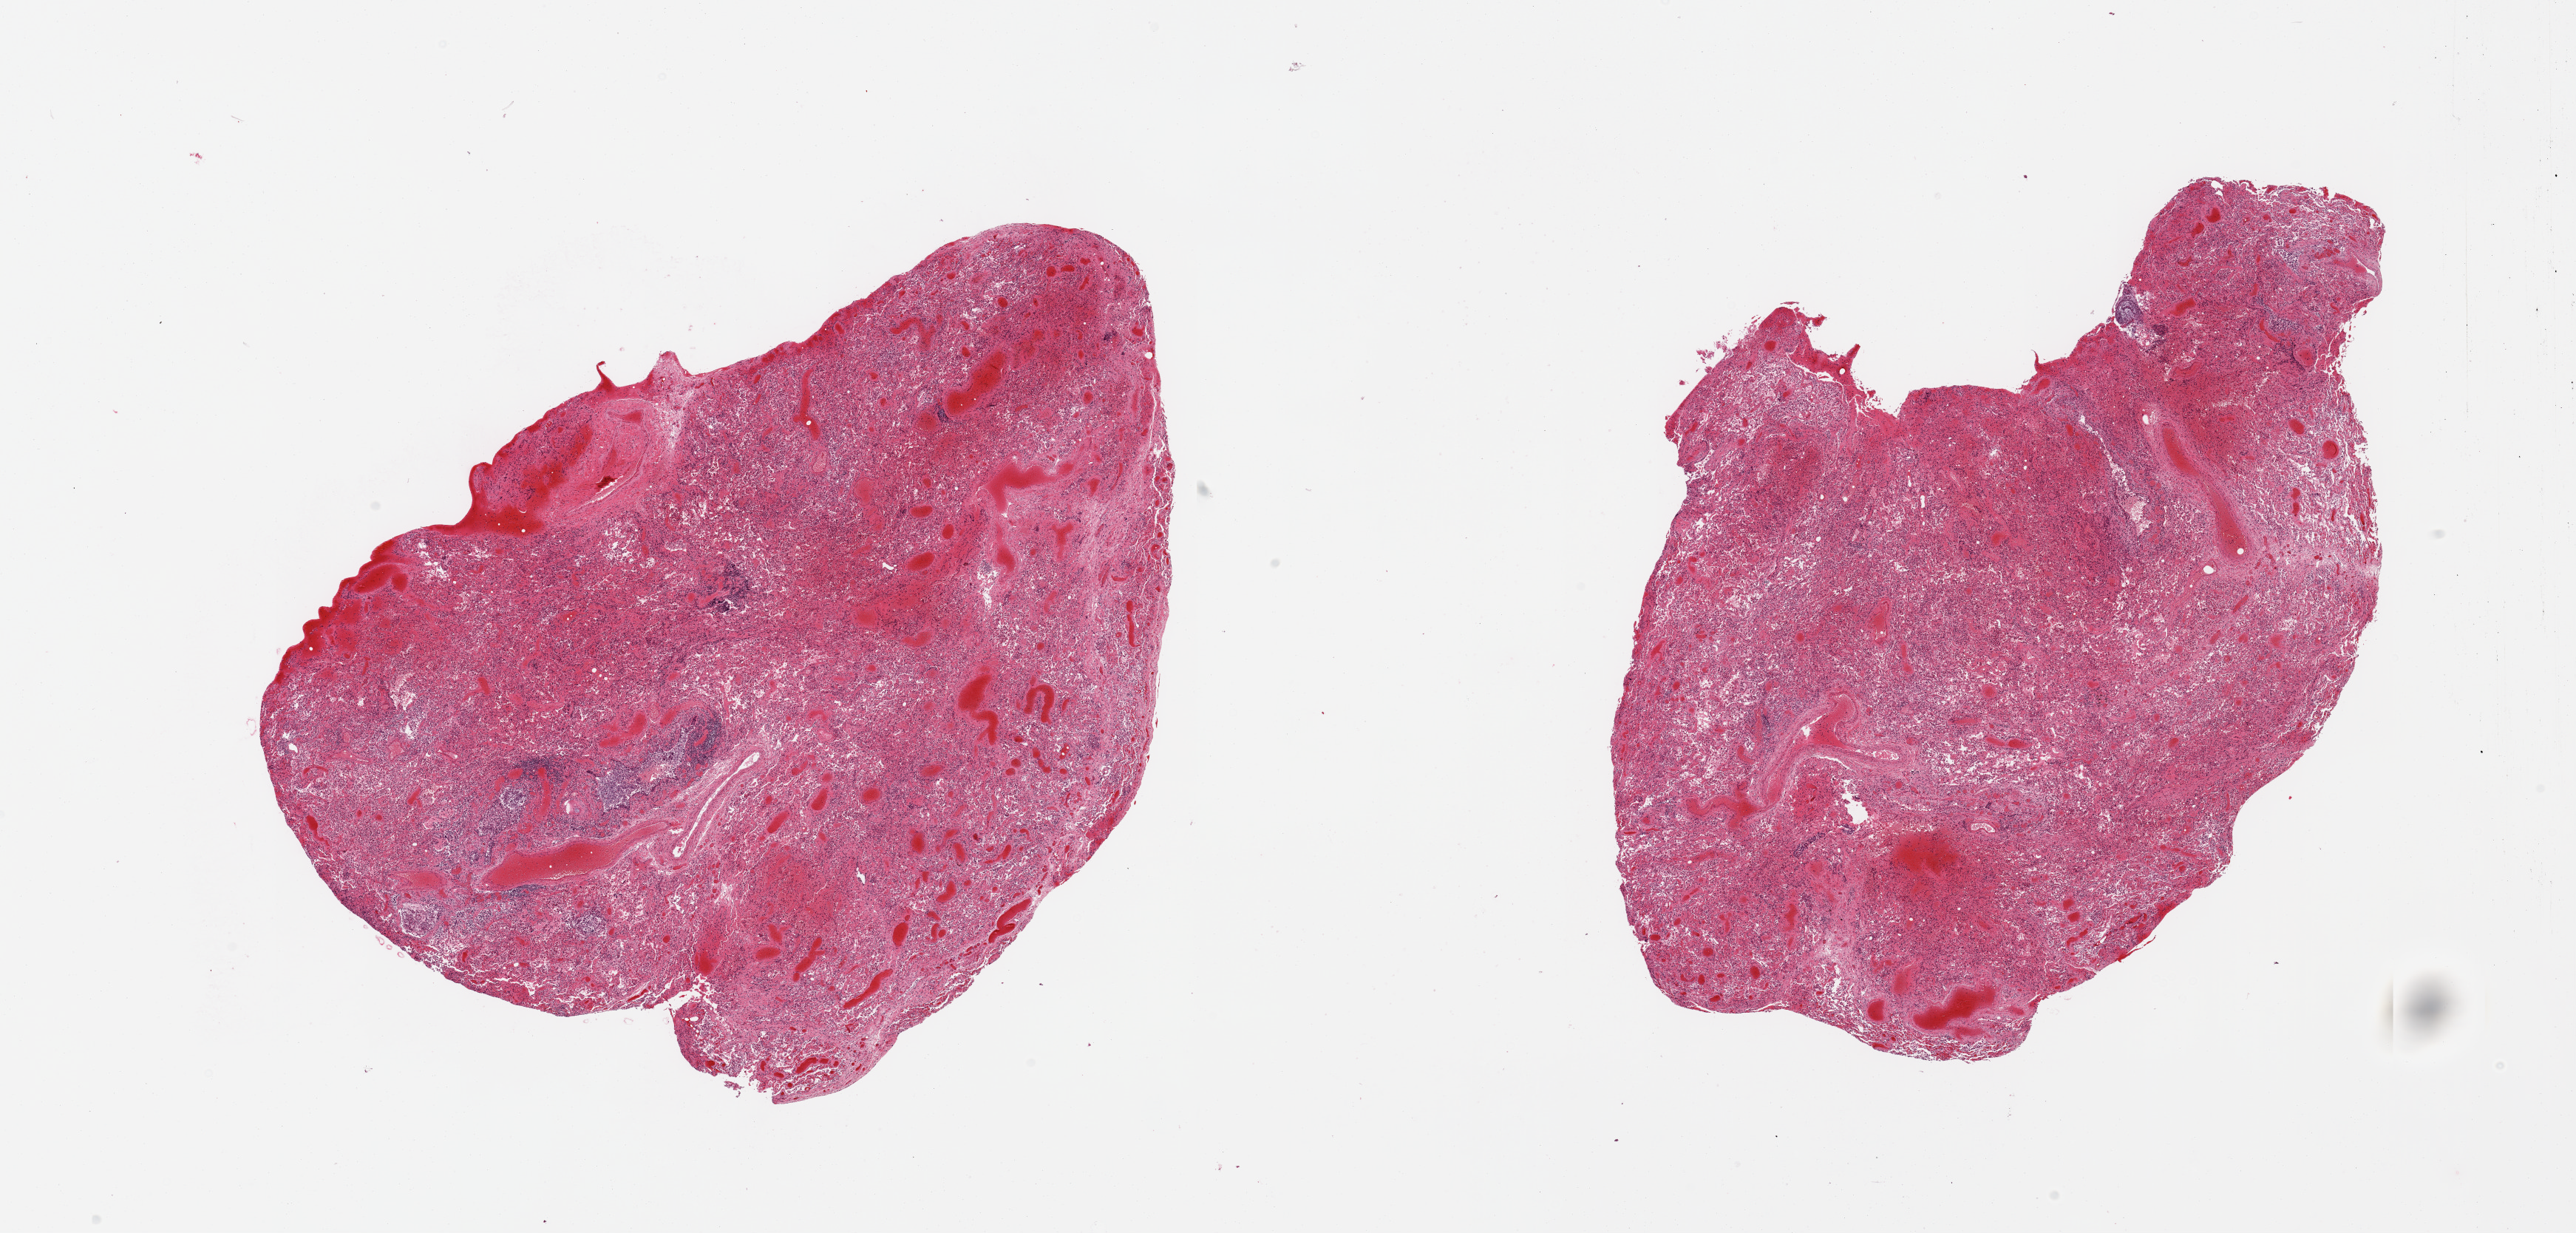
H&E whole-slide image, whole scanned area (about 27.6 x 13.2 mm, from a 20x scan) shown as a low-resolution overview. PAXgene-fixed paraffin-embedded (PFPE) section. Sampled site (target tissue): lung. Tissue donor sample. Female donor.
* review note (as recorded): 2 pieces; severe congestion with hemorrhage, generalized desquamation of bronchial and alveolar lining epithelium, collections of inflammatory cells